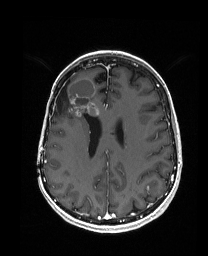
Brain MRI from a brain-tumour surgery series, one axial slice; T1-weighted post-contrast; 1 mm slice thickness; 208 × 256 image matrix, field of view 203 × 250 mm. Case-level facts recorded for this patient, not image findings: histopathology: Metastatic Carcinoma from Breast primary; tumour location: Right Frontal.
Structures marked on this image (expert manual segmentation):
- previous resection cavity: box from (x=53, y=80) to (x=70, y=114) px
- tumour: (x=55, y=77)–(x=104, y=128)